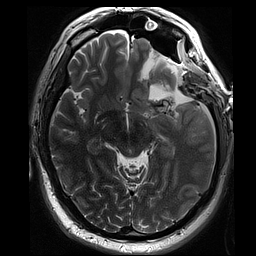
Brain MRI from a brain-tumour surgery series, one axial slice. Position 49 of 70 along the scan axis. 256 × 256 image matrix, field of view 220 × 220 mm. Case-level facts recorded for this patient, not image findings: histopathology: Oligodendroglioma; WHO grade: 3; IDH mutation: yes; tumour location: Left Sylvian Fissure (Temporal).
Structures marked on this image (expert manual segmentation):
- residual tumour: box from (x=168, y=97) to (x=174, y=103) px